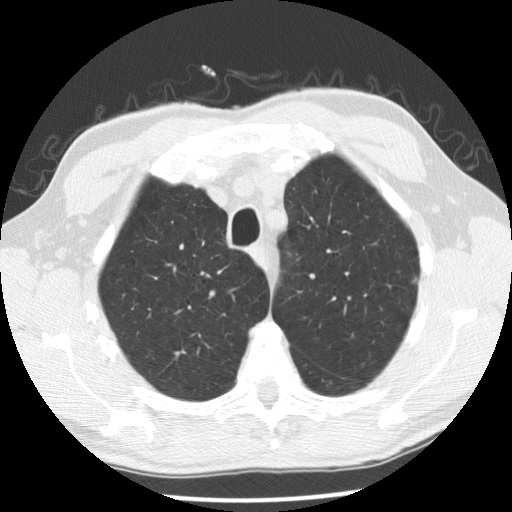
Low-dose screening chest CT, axial slice. Second screening round (one year after baseline). Lung window (W 1500 / L -600 HU). Standard (soft-tissue) reconstruction kernel (STANDARD). 120 kVp. Slice 33 of 173 in the series. Male participant, aged 63 years at enrolment. Current smoker at enrolment.
Expert reader's lesion annotation, bounding box (x1, y1, x2, y2) in pixels: (394, 263, 433, 299). The exam's reader record, not a measurement of the box and not confirmed to be the same lesion: non-calcified nodule or mass ≥4 mm, left upper lobe, 5 × 3 mm, poorly defined margins, soft tissue attenuation, pre-existing on the prior screen: yes; interval growth: no. Official screen result: positive, no significant change: stable abnormalities potentially related to lung cancer, unchanged since the prior screening exam. Participant outcome: lung cancer diagnosed 445 days after this screen — adenocarcinoma, NOS, left upper lobe, well differentiated (G1), stage IB (AJCC 6th edition), 5 mm at pathology.